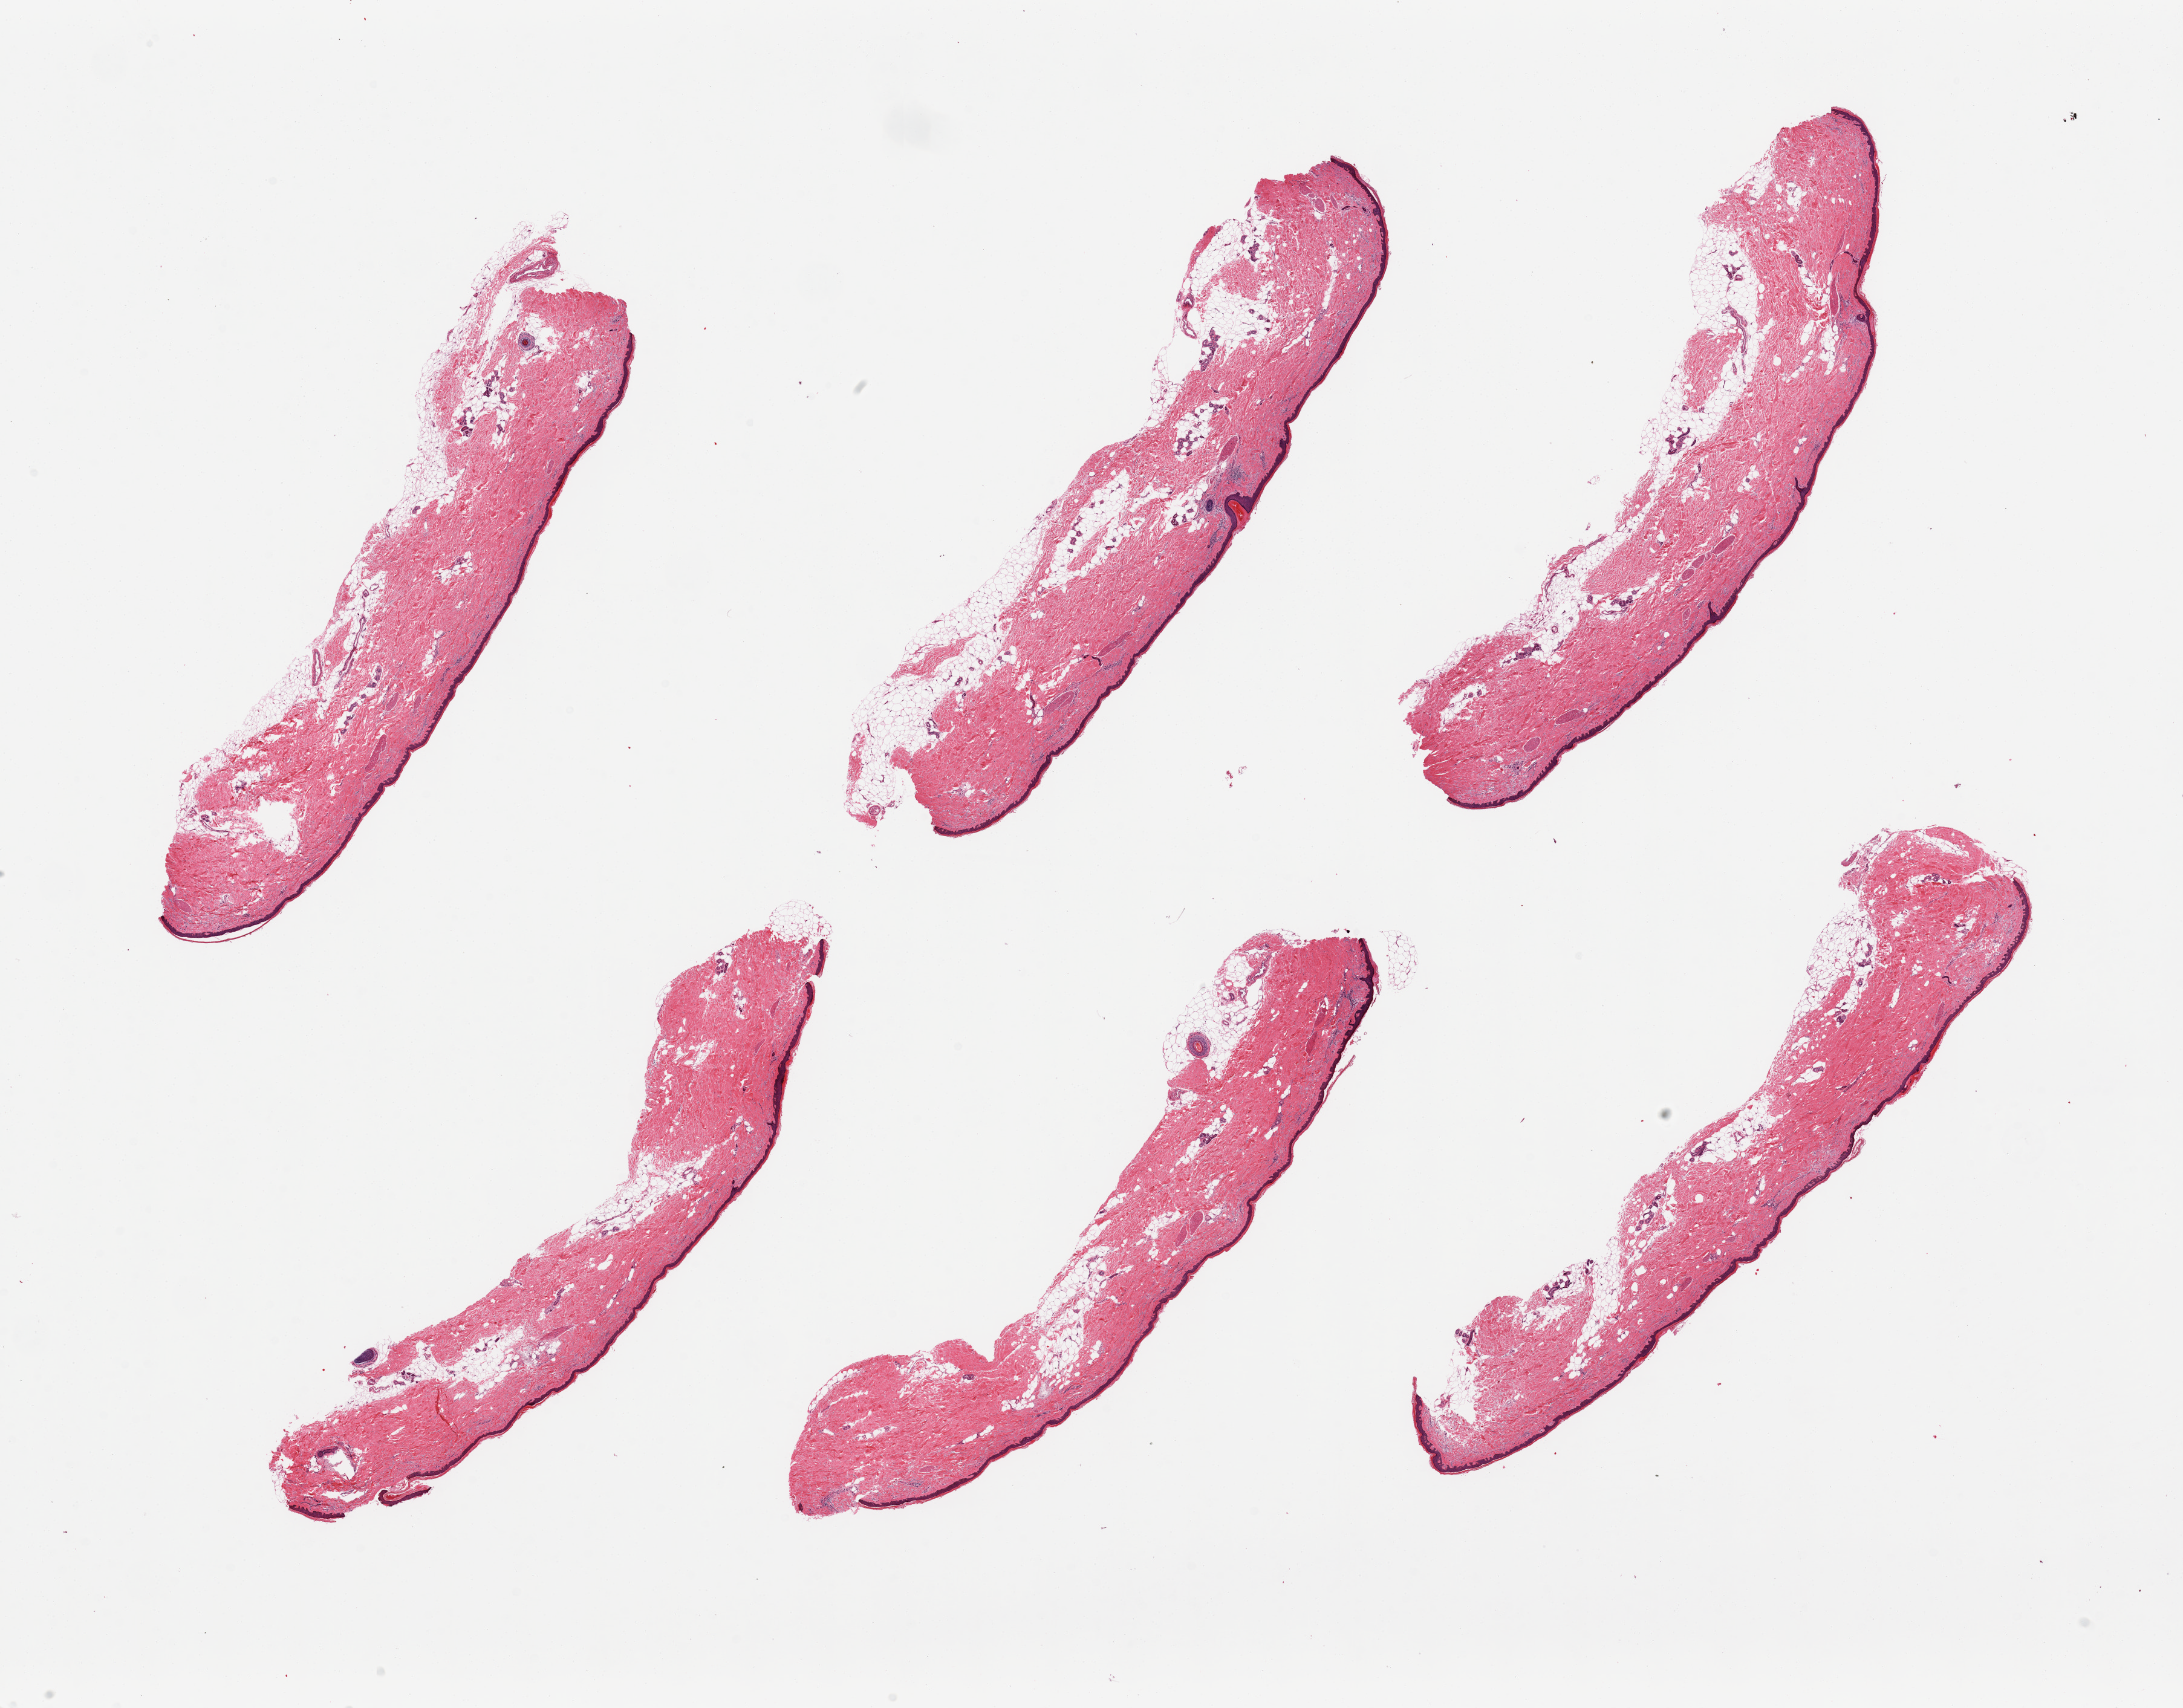
Whole-slide image, H&E stain, brightfield, a low-resolution overview of the entire scanned area, about 28.5 x 22.3 mm (from a 20x scan); PAXgene-fixed, paraffin-embedded tissue; target tissue: skin of lower leg; donor tissue sample. Male donor.
Pathologist's review note for this sample: 6 pieces, include 5-10% attached and internal adipose tissue, squamous epithelium measures 40-50 microns.